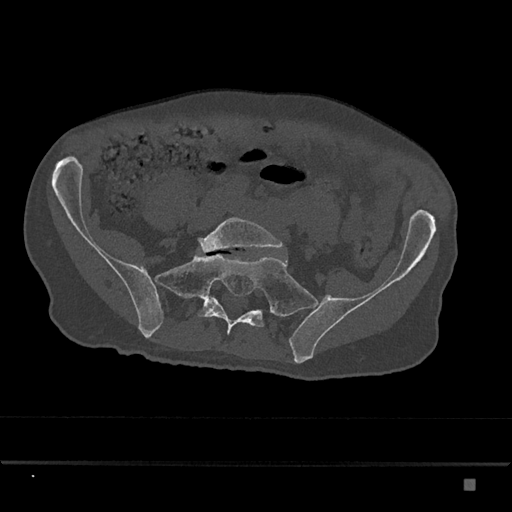
CT including the spine, one axial slice; 120 kVp; bone window (W 1800 / L 400 HU); 512 × 512 image matrix, field of view 390 × 390 mm. Male patient, age 72 years. From the clinical record (not read from this slice): primary cancer: prostate.
Structures marked on this image (semi-automatic segmentation, software-assisted and operator-edited):
- L5 vertebra: bounding box (x1, y1, x2, y2) in pixels: (198, 217, 283, 253)